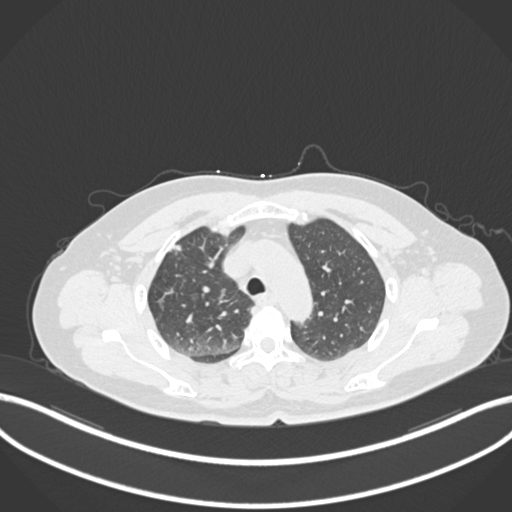
Chest CT, one axial slice; position 175 of 223 along the scan axis; reconstruction kernel B30f; 120 kVp; lung window (W 1500 / L -600 HU); 512 × 512 image matrix, field of view 400 × 400 mm. Patient: female, 56 years. From the clinical record (not read from this slice): clinical TNM (as recorded): T1c N0 M0.
Outlined on this slice (rectangle marked by the reading radiologist):
- lung tumour (recorded histology: adenocarcinoma): bounding box <171,238,183,255> (left, top, right, bottom; pixels)